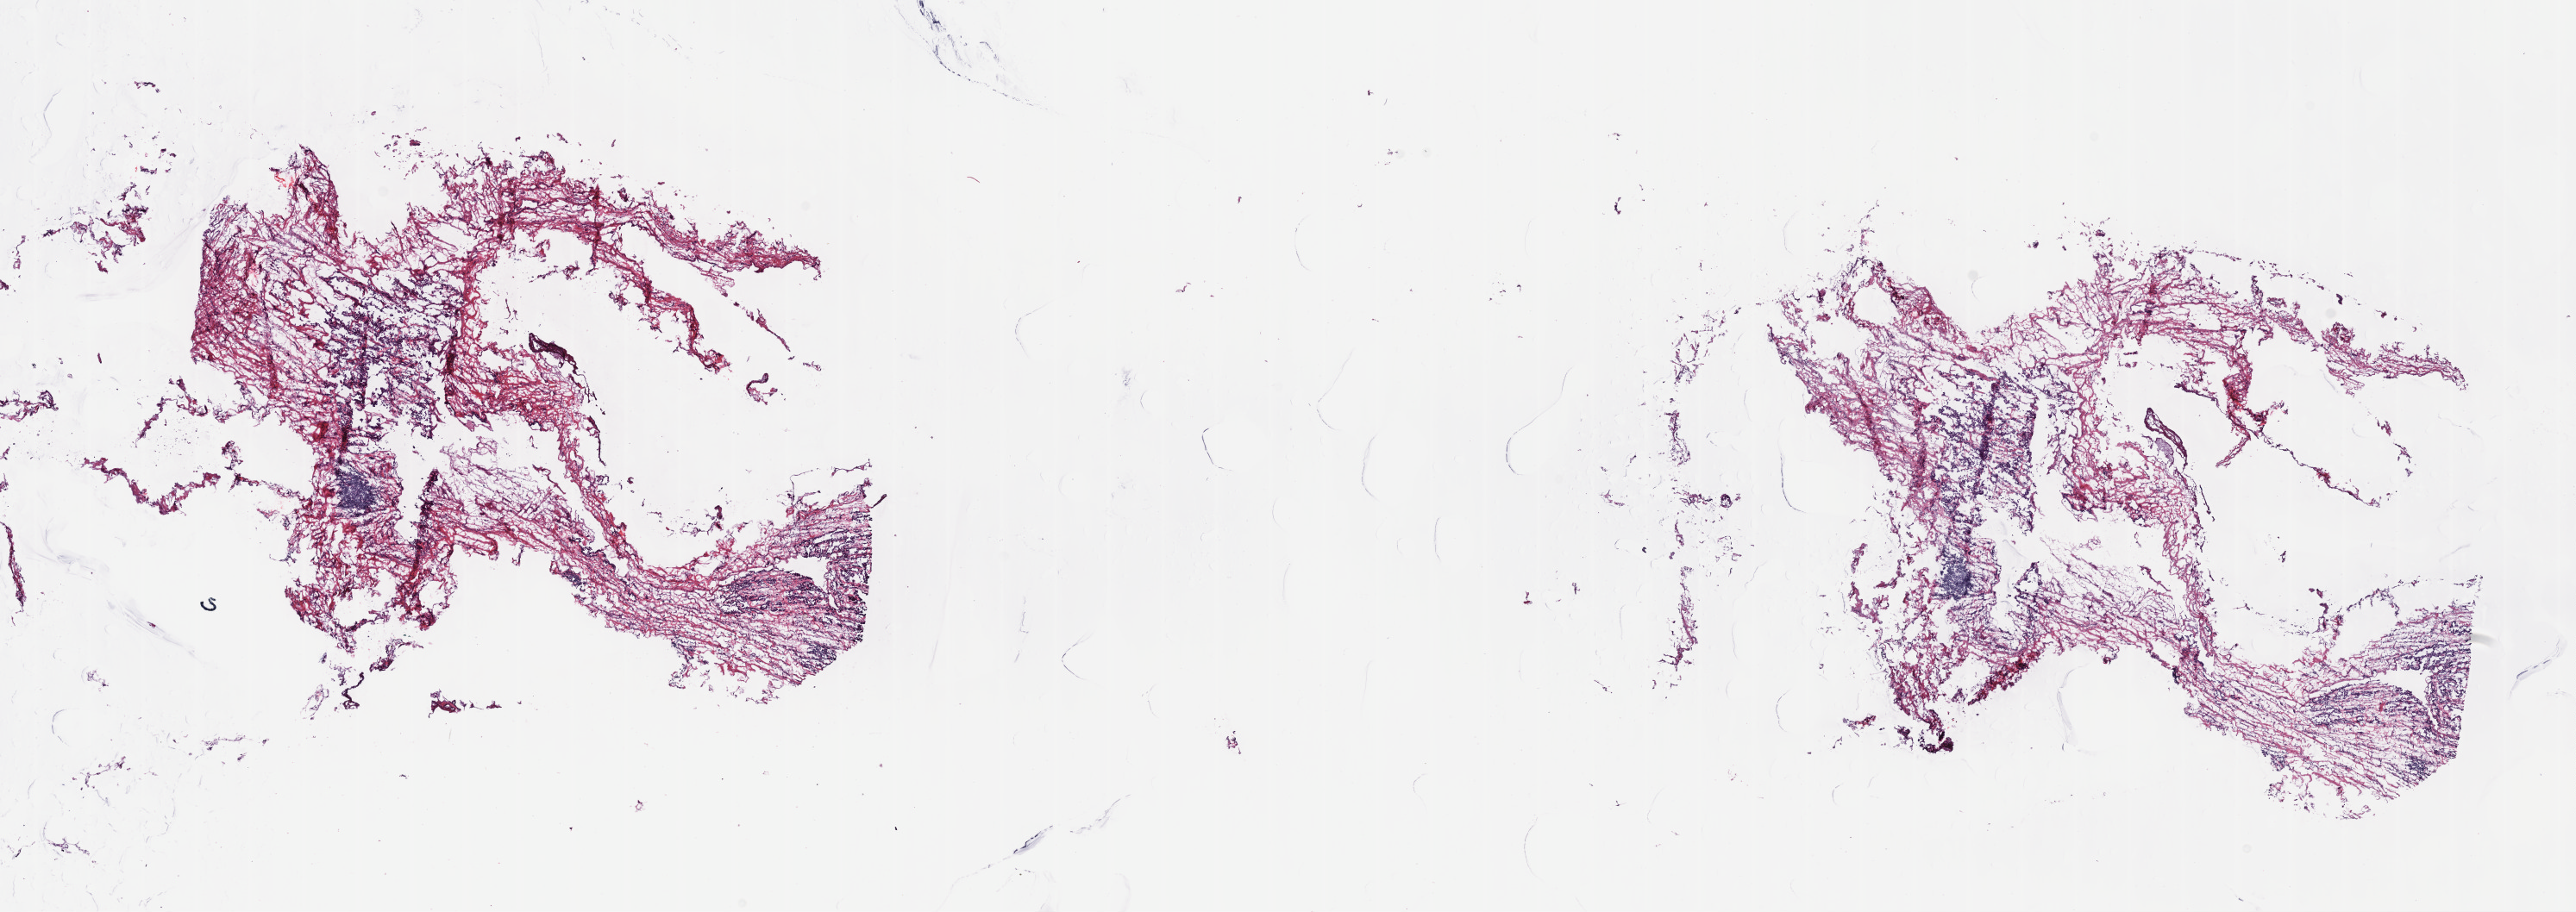
H&E whole-slide image, a low-resolution overview of the entire scanned area, about 24.2 x 8.6 mm (acquisition: 40x scan); frozen section from the top of the tissue portion; primary tumour sample from the mesothelium. Male, age 77 years at initial diagnosis. Pathologist review of this section (percent, as recorded): tumour cells 60%, tumour nuclei 60%, normal cells 0%, stromal cells 30%, necrosis 10%. Inflammatory infiltration, as recorded: lymphocyte infiltration 40%, monocyte infiltration 20%, neutrophil infiltration 20%.
- pathologic diagnosis: Epithelioid mesothelioma, malignant (pleura, NOS)
- laterality: right
- AJCC pathologic stage: IA (7th edition)